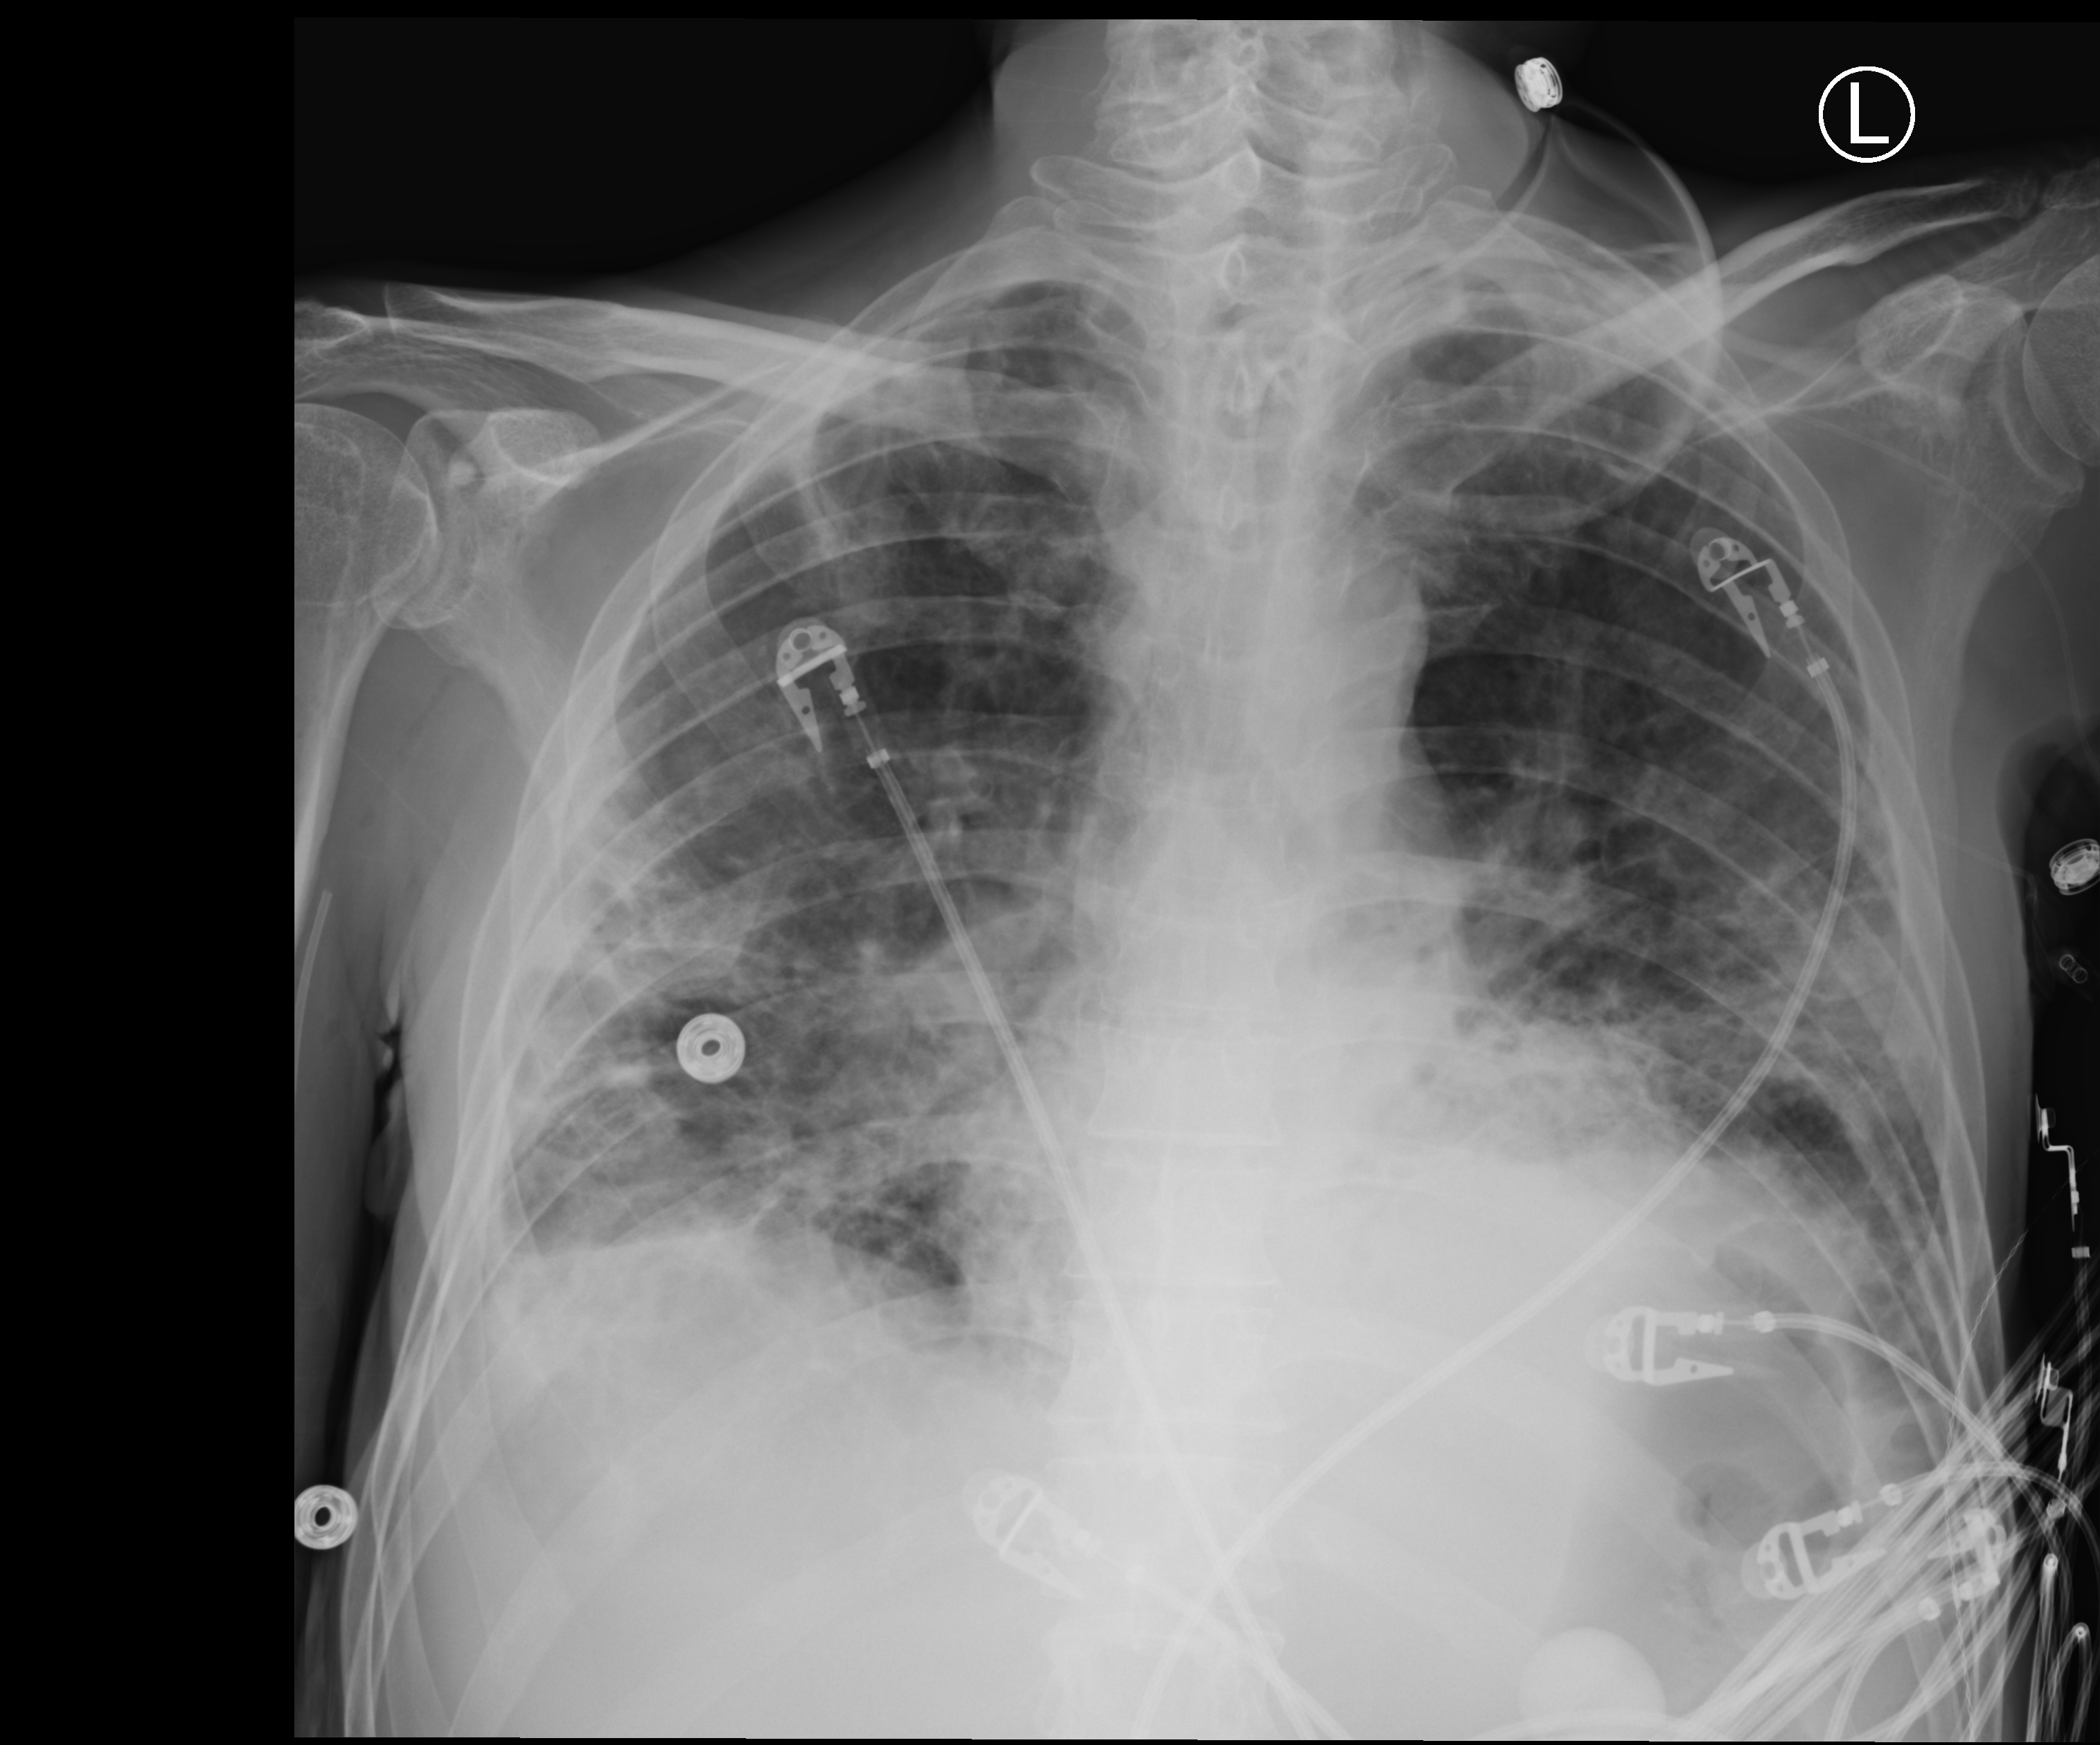
Bedside chest radiograph (computed radiography), anteroposterior (AP) projection. Patient hospitalised with COVID-19; male, aged 18–59 years.
Hospital-stay facts (about this admission, not read from this image; timing relative to this image not recorded): mechanically ventilated during this hospital stay: yes.